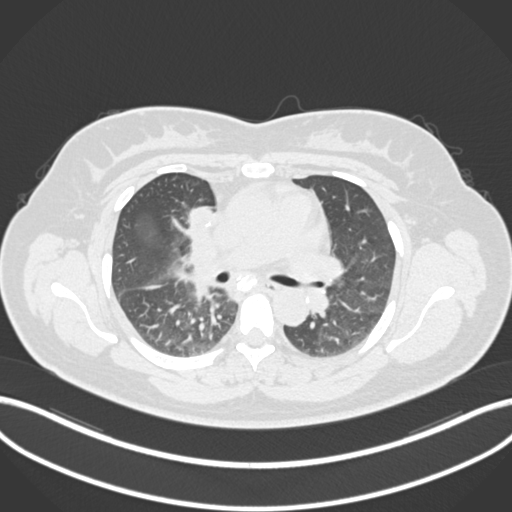
Chest CT, one axial slice. Slice 103 of 183 in the series (ordered by position). Reconstruction kernel B30f. 120 kVp. Lung window (W 1500 / L -600 HU). 1 mm slice thickness. 512 × 512 image matrix, field of view 400 × 400 mm. Patient: female, 46 years. Case-level facts recorded for this patient, not image findings: clinical TNM (as recorded): T2a N1 M0.
Structures marked on this image (rectangle marked by the reading radiologist):
- lung tumour (recorded histology: adenocarcinoma): bounding box (x1, y1, x2, y2) in pixels: (187, 202, 217, 231)